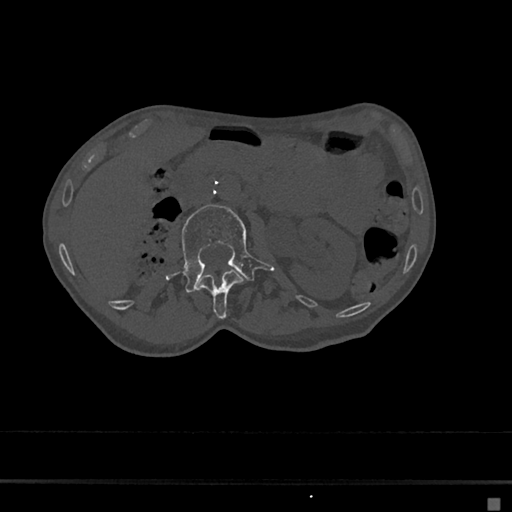
CT including the spine, one axial slice; slice 31 of 797 in the series (ordered by position); reconstruction kernel Br40s/3; bone window (W 1800 / L 400 HU); 0.5 mm slice thickness; 512 × 512 image matrix, field of view 360 × 360 mm. Patient: female, 68 years. Case-level facts recorded for this patient, not image findings: primary cancer: renal.
Annotated regions visible in this slice (semi-automatic segmentation, software-assisted and operator-edited):
- L1 vertebra: box from (x=196, y=269) to (x=244, y=319) px
- L2 vertebra: (x=166, y=204)–(x=274, y=292)